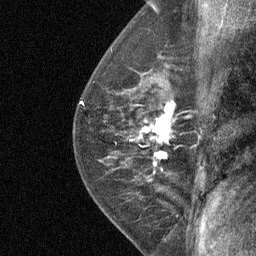
Breast MRI (dynamic contrast-enhanced), one sagittal slice; slice 42 of 64 in the series (ordered by position); dynamic contrast-enhanced study with each time point stored as its own series, time point 2 of 4 at this slice position (early post-contrast, ordered by acquisition time); 1.5 T; TE 4.8 ms, TR 27 ms; 2 mm slice thickness; 256 × 256 image matrix, field of view 180 × 180 mm. Female patient, age 50 years. Case-level facts recorded for this patient, not image findings: setting: breast cancer imaged before/during neoadjuvant chemotherapy; receptor status: HER2-positive.
Outlined on this slice (semi-automatic segmentation, software-assisted and operator-edited):
- analysis volume of interest (the breast-tissue region the enhancement analysis was run in; not a lesion): bounding box <123,91,178,177> (left, top, right, bottom; pixels)
- tumour enhancement mask (voxels above the 90 % enhancement threshold inside the analysis volume of interest): <139,101,175,164>